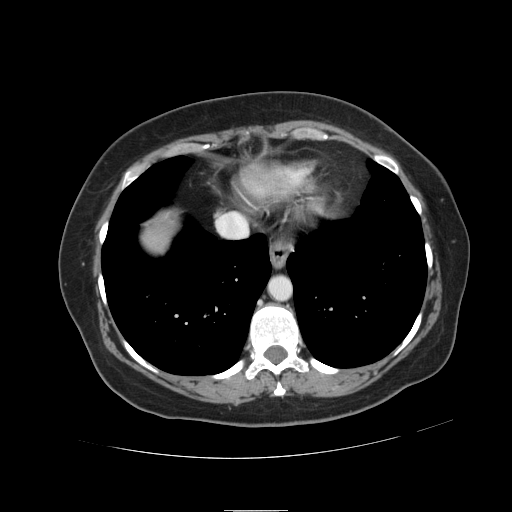
Contrast-enhanced abdominal CT, one axial slice; slice 113 of 121 in the series (ordered by position); 120 kVp; intravenous contrast given; soft-tissue window (W 400 / L 40 HU); 2.5 mm slice thickness; 512 × 512 image matrix, field of view 400 × 400 mm. Female patient, age 52 years. Case-level facts recorded for this patient, not image findings: diagnosis: colorectal cancer liver metastases, imaged before liver resection; multiple liver metastases: yes; largest metastasis: 6.3 cm; disease in both lobes: no.
Annotated regions visible in this slice (manually delineated by an expert):
- liver: bounding box (x1, y1, x2, y2) in pixels: (144, 221, 172, 251)